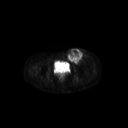
FDG PET of an extremity soft-tissue mass (from a PET/CT study), one axial slice; position 68 of 267 along the scan axis; 128 × 128 image matrix. Patient: female, 24 years. Case-level facts recorded for this patient, not image findings: histological type: leiomyosarcoma; grade: high; site of the primary tumour: groin.
Annotated regions visible in this slice (expert contour drawn on MRI and transferred to this co-registered scan by the dataset authors):
- gross tumour volume including surrounding oedema: box from (x=66, y=48) to (x=90, y=65) px
- gross tumour volume (mass): (x=66, y=49)–(x=83, y=64)